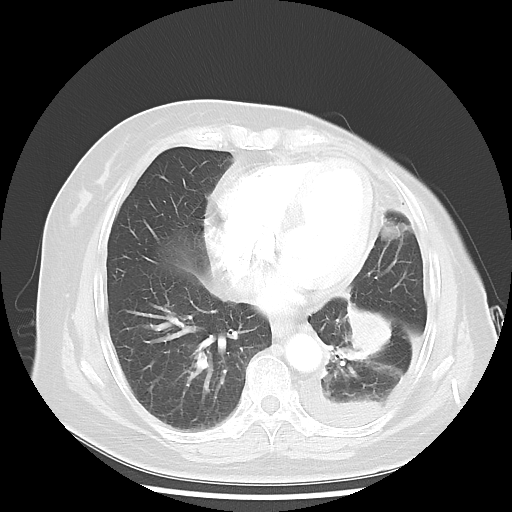
Chest CT, one axial slice; slice 16 of 48 in the series (ordered by position); reconstruction kernel LUNG; lung window (W 1500 / L -600 HU); 5 mm slice thickness; 512 × 512 image matrix. Patient: female, 63 years. Case-level facts recorded for this patient, not image findings: clinical TNM (as recorded): T2 N0 M1.
Outlined on this slice (rectangle marked by the reading radiologist):
- lung tumour (recorded histology: adenocarcinoma): box from (x=339, y=290) to (x=393, y=368) px